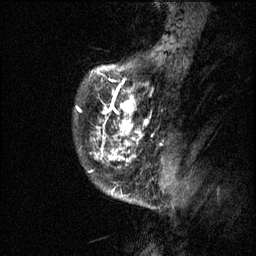
Breast MRI (dynamic contrast-enhanced), one sagittal slice; position 10 of 60 along the scan axis; 3 images stored at this slice position (order not interpretable as contrast timing); 1.5 T; TE 4.2 ms, TR 11.1 ms; 2 mm slice thickness; 256 × 256 image matrix. Patient: female, 50 years.
Structures marked on this image (semi-automatically segmented with operator editing):
- analysis volume of interest (the breast-tissue region the enhancement analysis was run in; not a lesion): bounding box [x1, y1, x2, y2] px = [74, 68, 153, 141]
- tumour enhancement mask (voxels above the 70 % enhancement threshold inside the analysis volume of interest): [76, 68, 145, 141]